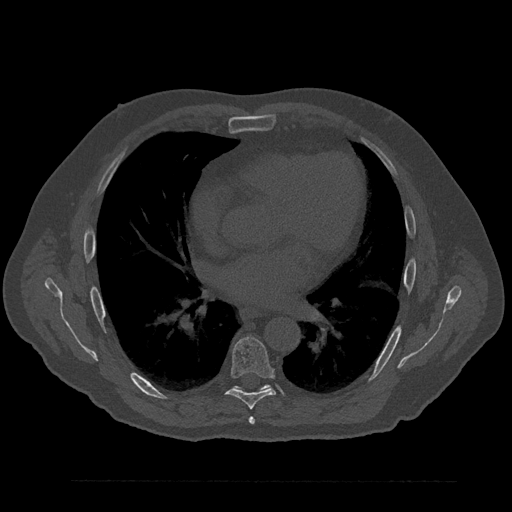
CT including the spine, one axial slice. Position 499 of 797 along the scan axis. Bone window (W 1800 / L 400 HU). 0.5 mm slice thickness. 512 × 512 image matrix, field of view 430 × 430 mm. Male patient, age 61 years. From the clinical record (not read from this slice): primary cancer: prostate.
Outlined on this slice (semi-automatically segmented with operator editing):
- T6 vertebra: bounding box (x1, y1, x2, y2) in pixels: (249, 416, 255, 425)
- T7 vertebra: (226, 337, 276, 410)
- T8 vertebra: (233, 384, 270, 390)